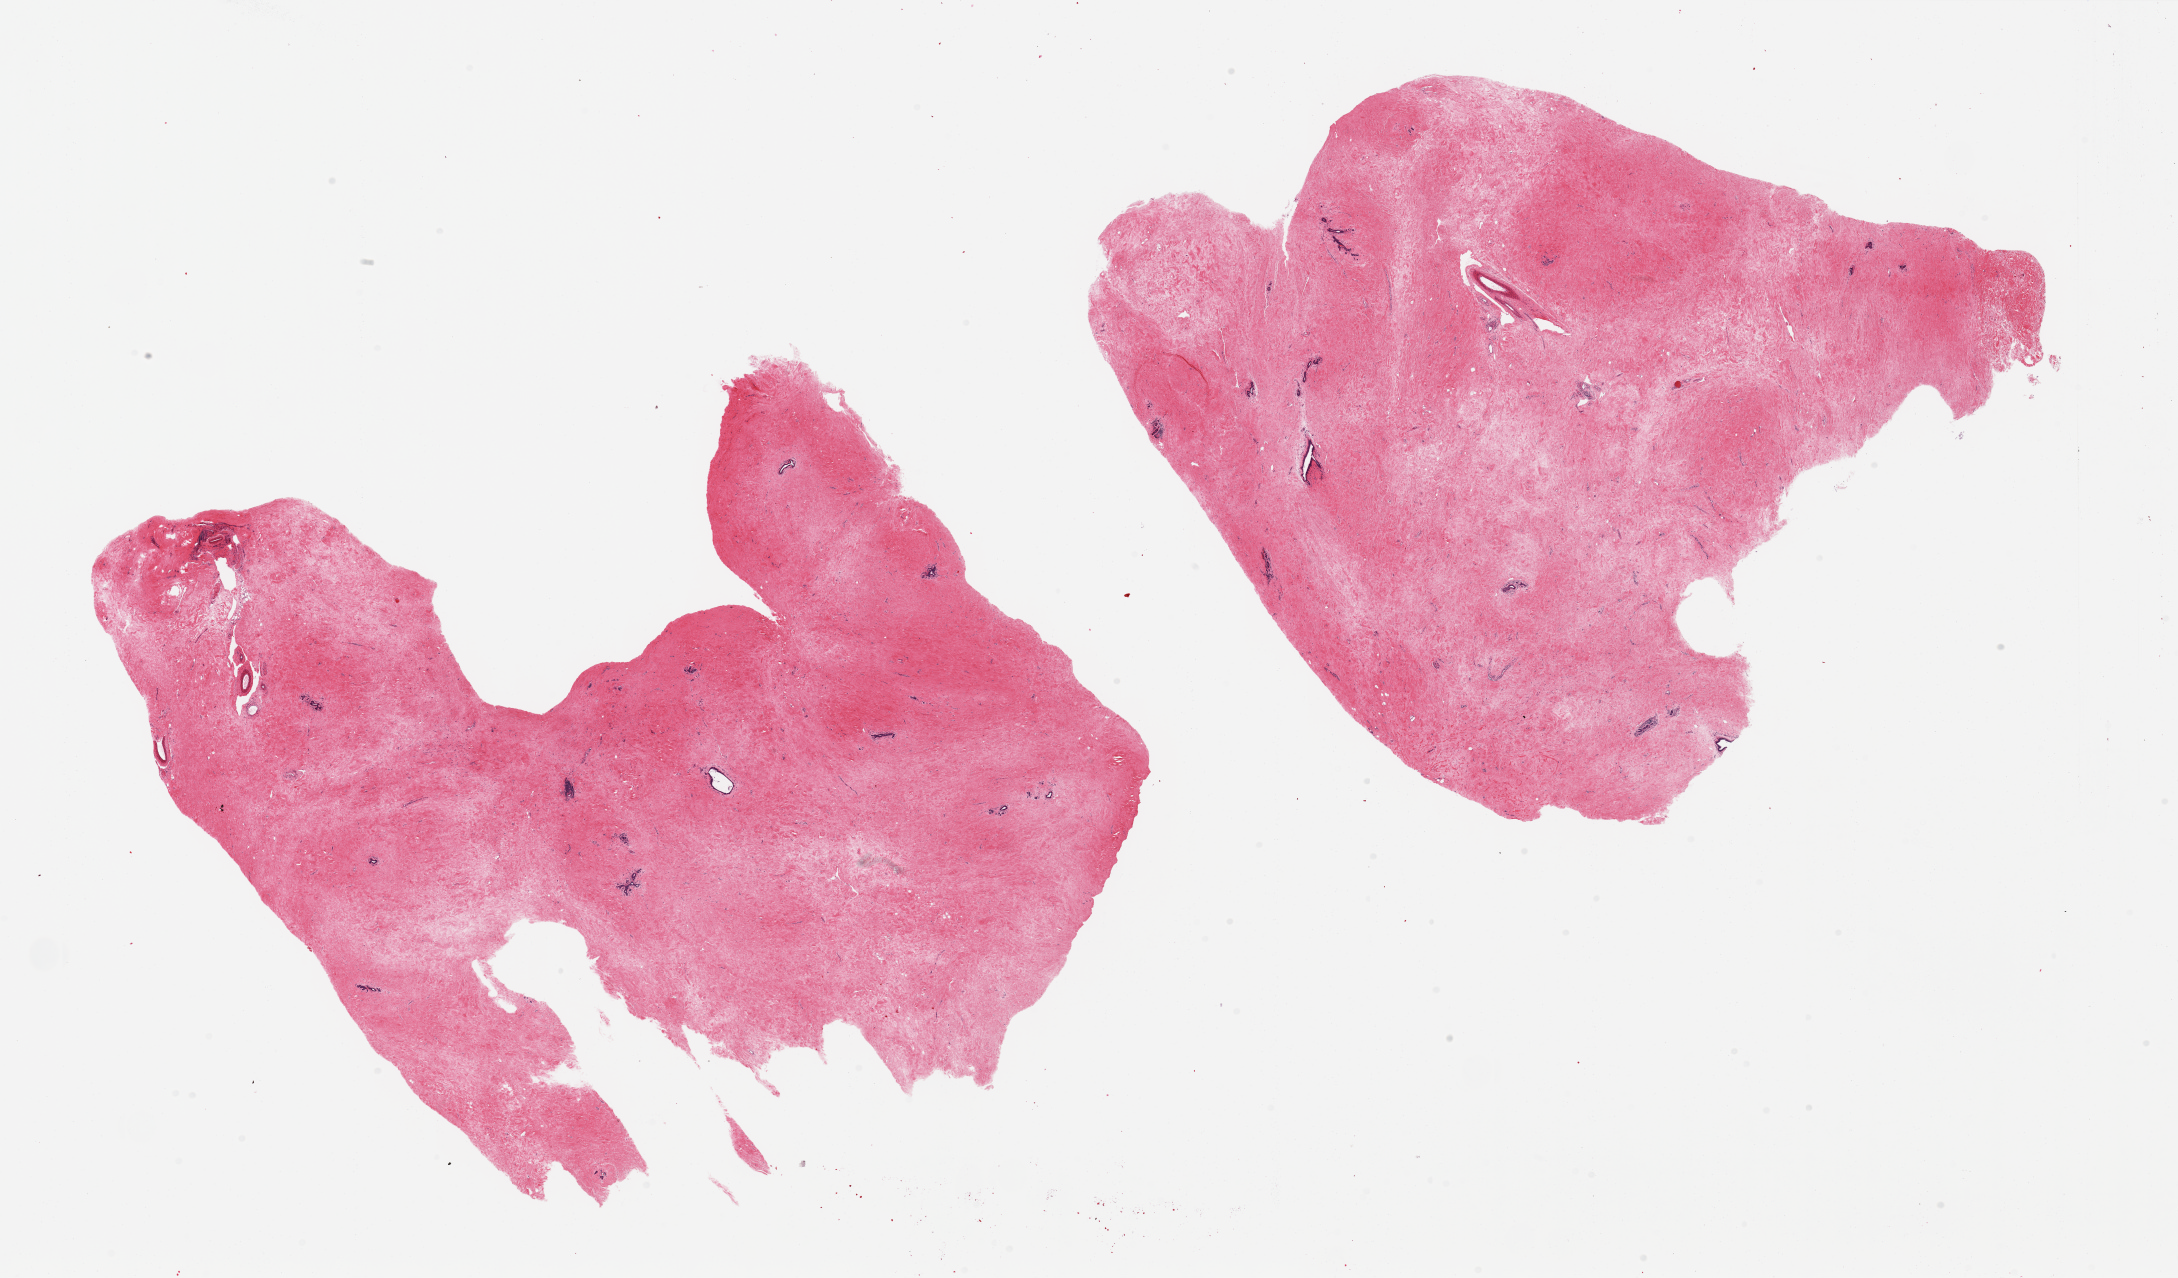
Whole-slide image, H&E stain, brightfield, whole scanned area (about 34.5 x 20.2 mm, from a 20x scan) shown as a low-resolution overview, PAXgene-fixed paraffin-embedded (PFPE) section, sampled site (target tissue): breast, donor tissue sample.
- reviewer comment on this tissue sample: 2 pieces, marked stromal fibrous mastopathy, rare ductal/lobular elements, atrophic for age